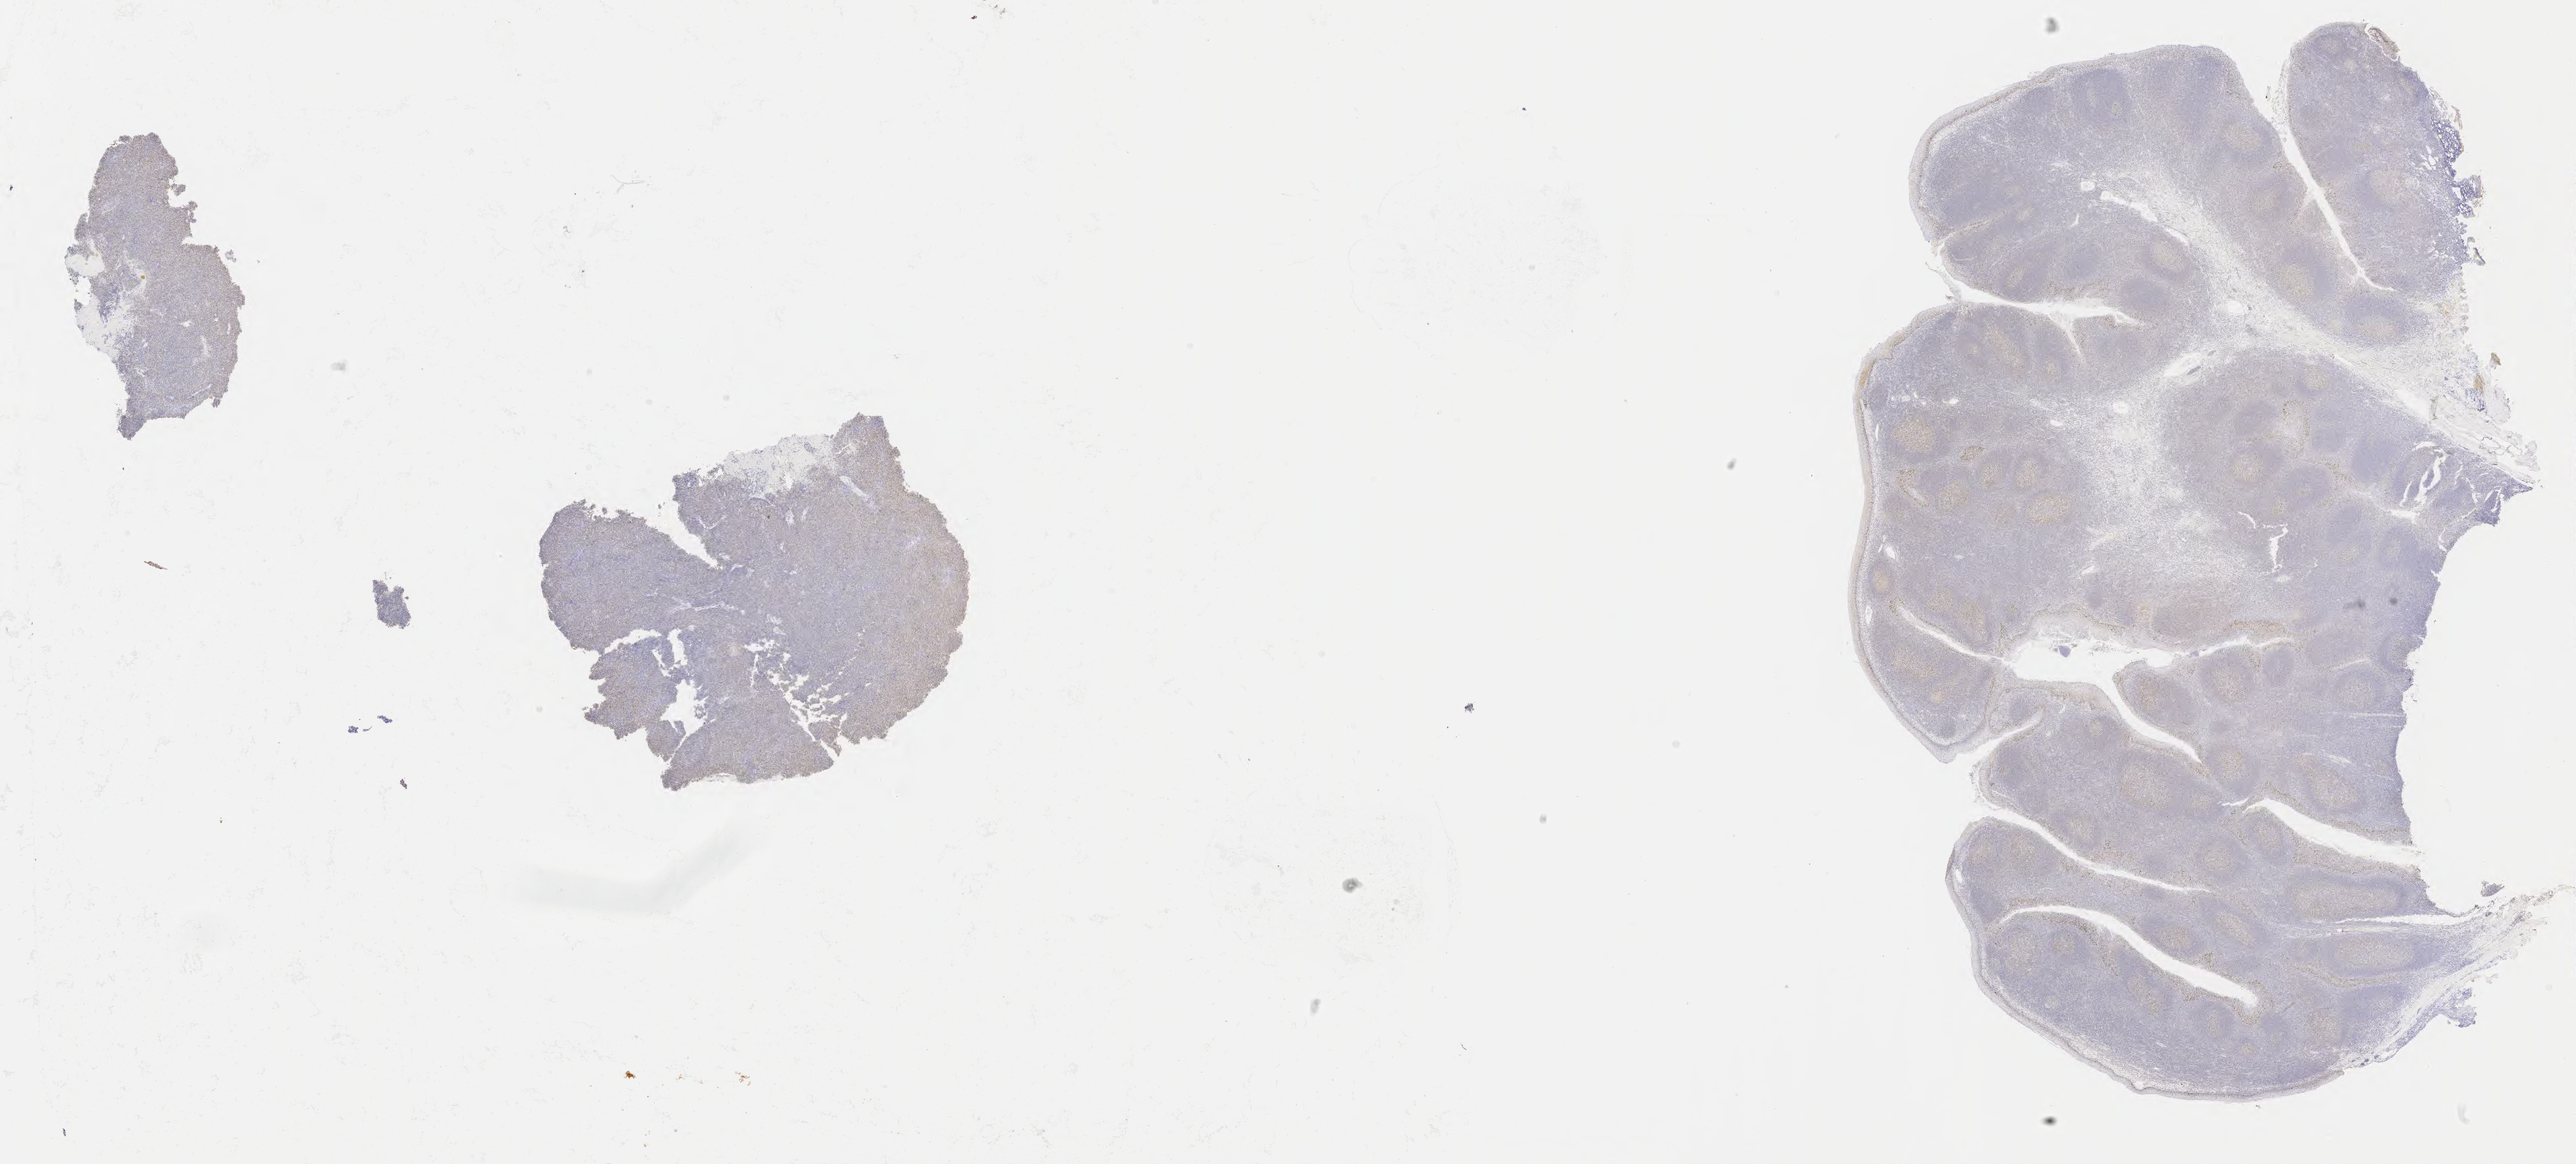
IHC for p53, whole-slide image — whole scanned area (about 30.7 x 13.9 mm) shown as a low-resolution overview, tumor tissue, anatomic site: lymph node. Patient female; age 51 years.
Diagnosis: Diffuse large B-cell lymphoma, NOS.